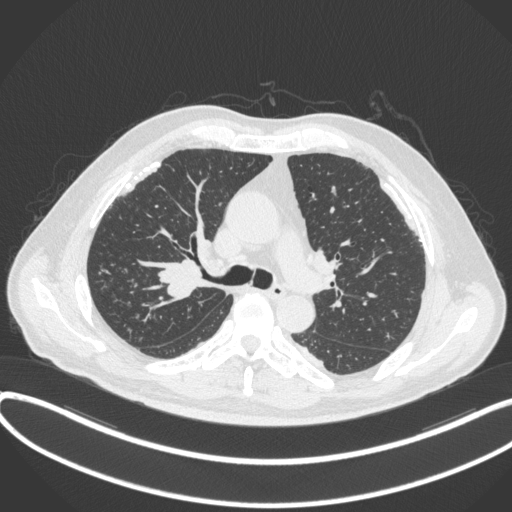
Chest CT, one axial slice; reconstruction kernel B31f; 120 kVp; lung window (W 1500 / L -600 HU); 1 mm slice thickness; 512 × 512 image matrix, field of view 400 × 400 mm. Male patient, age 58 years. Case-level facts recorded for this patient, not image findings: clinical TNM (as recorded): T1c N0 M0.
Outlined on this slice (rectangle marked by the reading radiologist):
- lung tumour (recorded histology: squamous cell carcinoma): box from (x=150, y=251) to (x=207, y=303) px